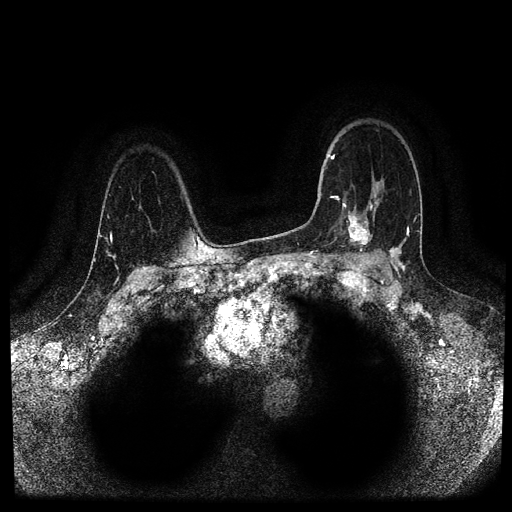
Breast MRI (dynamic contrast-enhanced, multi-phase), one axial slice; slice 75 of 116 in the series (ordered by position); dynamic contrast-enhanced series, time point 2 of 5 at this slice position (early post-contrast); 1.5 T; TE 2.6 ms, TR 5.3 ms; 2 mm slice thickness; 512 × 512 image matrix, field of view 350 × 350 mm. Female patient, age 44 years.
Outlined on this slice (semi-automatically segmented with operator editing):
- breast lesion (labelled 'tumour' in the annotation; benign lesions carry a separate 'benign' label): bounding box <341,207,374,255> (left, top, right, bottom; pixels)